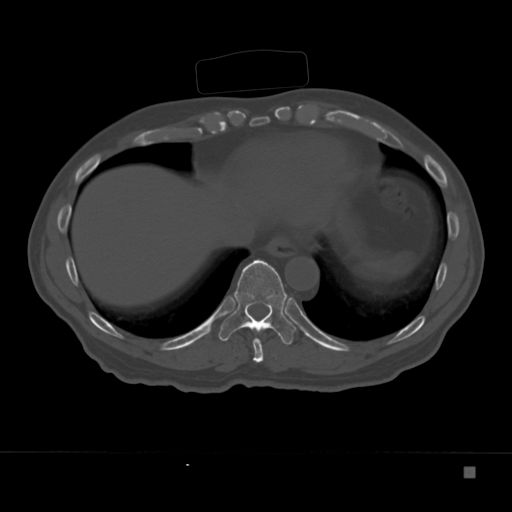
CT including the spine, one axial slice. Position 176 of 332 along the scan axis. 120 kVp. Bone window (W 1800 / L 400 HU). 1.5 mm slice thickness. 512 × 512 image matrix. Patient: male, 72 years. Case-level facts recorded for this patient, not image findings: primary cancer: skeletal.
Outlined on this slice (semi-automatically segmented with operator editing):
- T10 vertebra: box from (x=218, y=259) to (x=296, y=345) px
- T9 vertebra: (x=238, y=325)–(x=264, y=363)